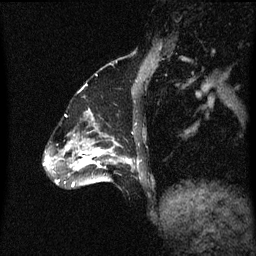
Breast MRI (dynamic contrast-enhanced), one sagittal slice; slice 18 of 60 in the series (ordered by position); dynamic contrast-enhanced series, image 2 of 3 at this slice position (ordered by acquisition); 1.5 T; TE 4.2 ms, TR 8.4 ms; 2 mm slice thickness; 256 × 256 image matrix, field of view 200 × 200 mm. Female patient, age 47 years.
Annotated regions visible in this slice (semi-automatically segmented with operator editing):
- analysis volume of interest (the breast-tissue region the enhancement analysis was run in; not a lesion): box from (x=85, y=138) to (x=140, y=185) px
- tumour enhancement mask (voxels above the 70 % enhancement threshold inside the analysis volume of interest): (x=85, y=148)–(x=132, y=181)